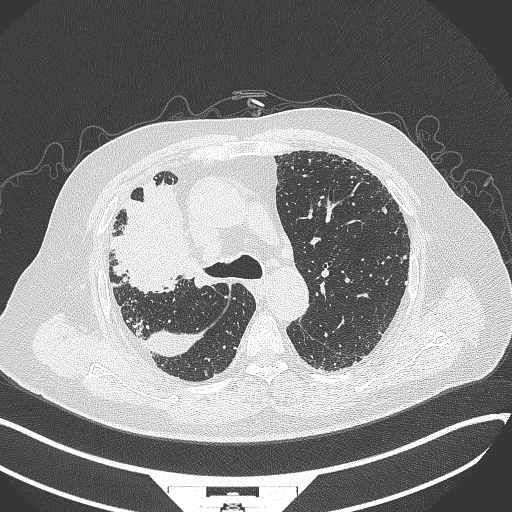
Chest CT, one axial slice. Position 237 of 384 along the scan axis. 120 kVp. Lung window (W 1500 / L -600 HU). 512 × 512 image matrix, field of view 400 × 400 mm. Patient: male, 69 years. From the clinical record (not read from this slice): clinical TNM (as recorded): T4 N3 M1.
Structures marked on this image (rectangle marked by the reading radiologist):
- lung tumour (recorded histology: adenocarcinoma): bounding box (x1, y1, x2, y2) in pixels: (103, 176, 187, 295)